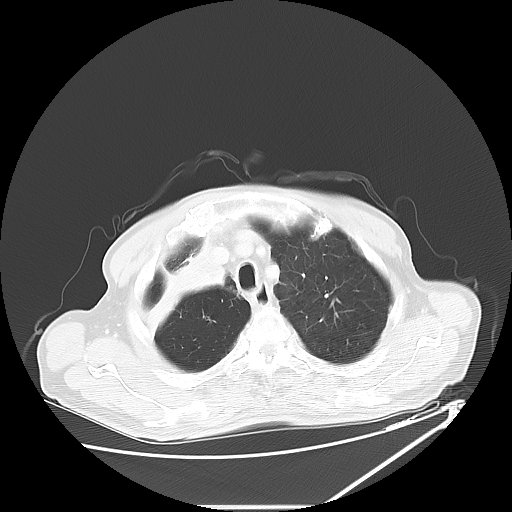
Chest CT, one axial slice. Position 51 of 60 along the scan axis. Reconstruction kernel LUNG. 120 kVp. Lung window (W 1500 / L -600 HU). 512 × 512 image matrix. Male patient, age 73 years. From the clinical record (not read from this slice): clinical TNM (as recorded): T2a N1 M0.
Outlined on this slice (rectangle marked by the reading radiologist):
- lung tumour (recorded histology: squamous cell carcinoma): bounding box (x1, y1, x2, y2) in pixels: (126, 241, 231, 336)